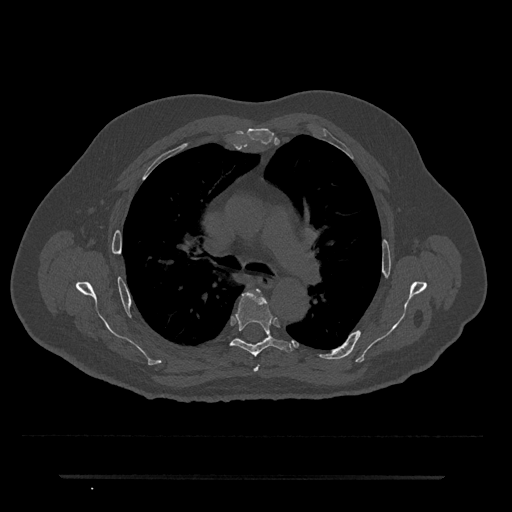
CT including the spine, one axial slice. Position 485 of 797 along the scan axis. 120 kVp. Bone window (W 1800 / L 400 HU). 512 × 512 image matrix. Male patient, age 69 years. Case-level facts recorded for this patient, not image findings: primary cancer: prostate.
Annotated regions visible in this slice (semi-automatic segmentation, software-assisted and operator-edited):
- T4 vertebra: bounding box (x1, y1, x2, y2) in pixels: (254, 290, 259, 372)
- T5 vertebra: (230, 290, 293, 357)